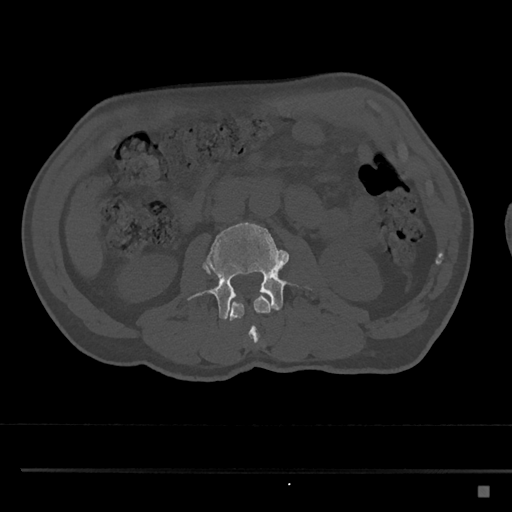
CT including the spine, one axial slice. Position 718 of 797 along the scan axis. 120 kVp. Bone window (W 1800 / L 400 HU). 0.5 mm slice thickness. 512 × 512 image matrix, field of view 391 × 391 mm. Patient: male, 59 years. From the clinical record (not read from this slice): primary cancer: prostate.
Outlined on this slice (semi-automatically segmented with operator editing):
- L2 vertebra: box from (x=206, y=271) to (x=272, y=343) px
- L3 vertebra: (x=187, y=222)–(x=312, y=320)